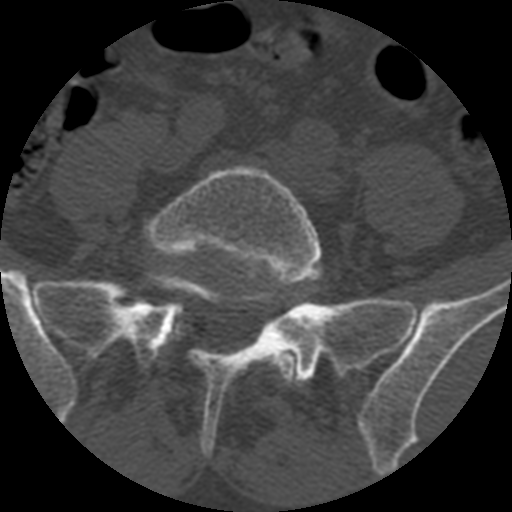
CT including the spine, one axial slice. Slice 246 of 399 in the series (ordered by position). Reconstruction kernel STANDARD. 120 kVp. Bone window (W 1800 / L 400 HU). 1.25 mm slice thickness. 512 × 512 image matrix, field of view 160 × 160 mm. Patient age 71 years. From the clinical record (not read from this slice): primary cancer: prostate.
Structures marked on this image (semi-automatic segmentation, software-assisted and operator-edited):
- L5 vertebra: bounding box <146,165,323,385> (left, top, right, bottom; pixels)